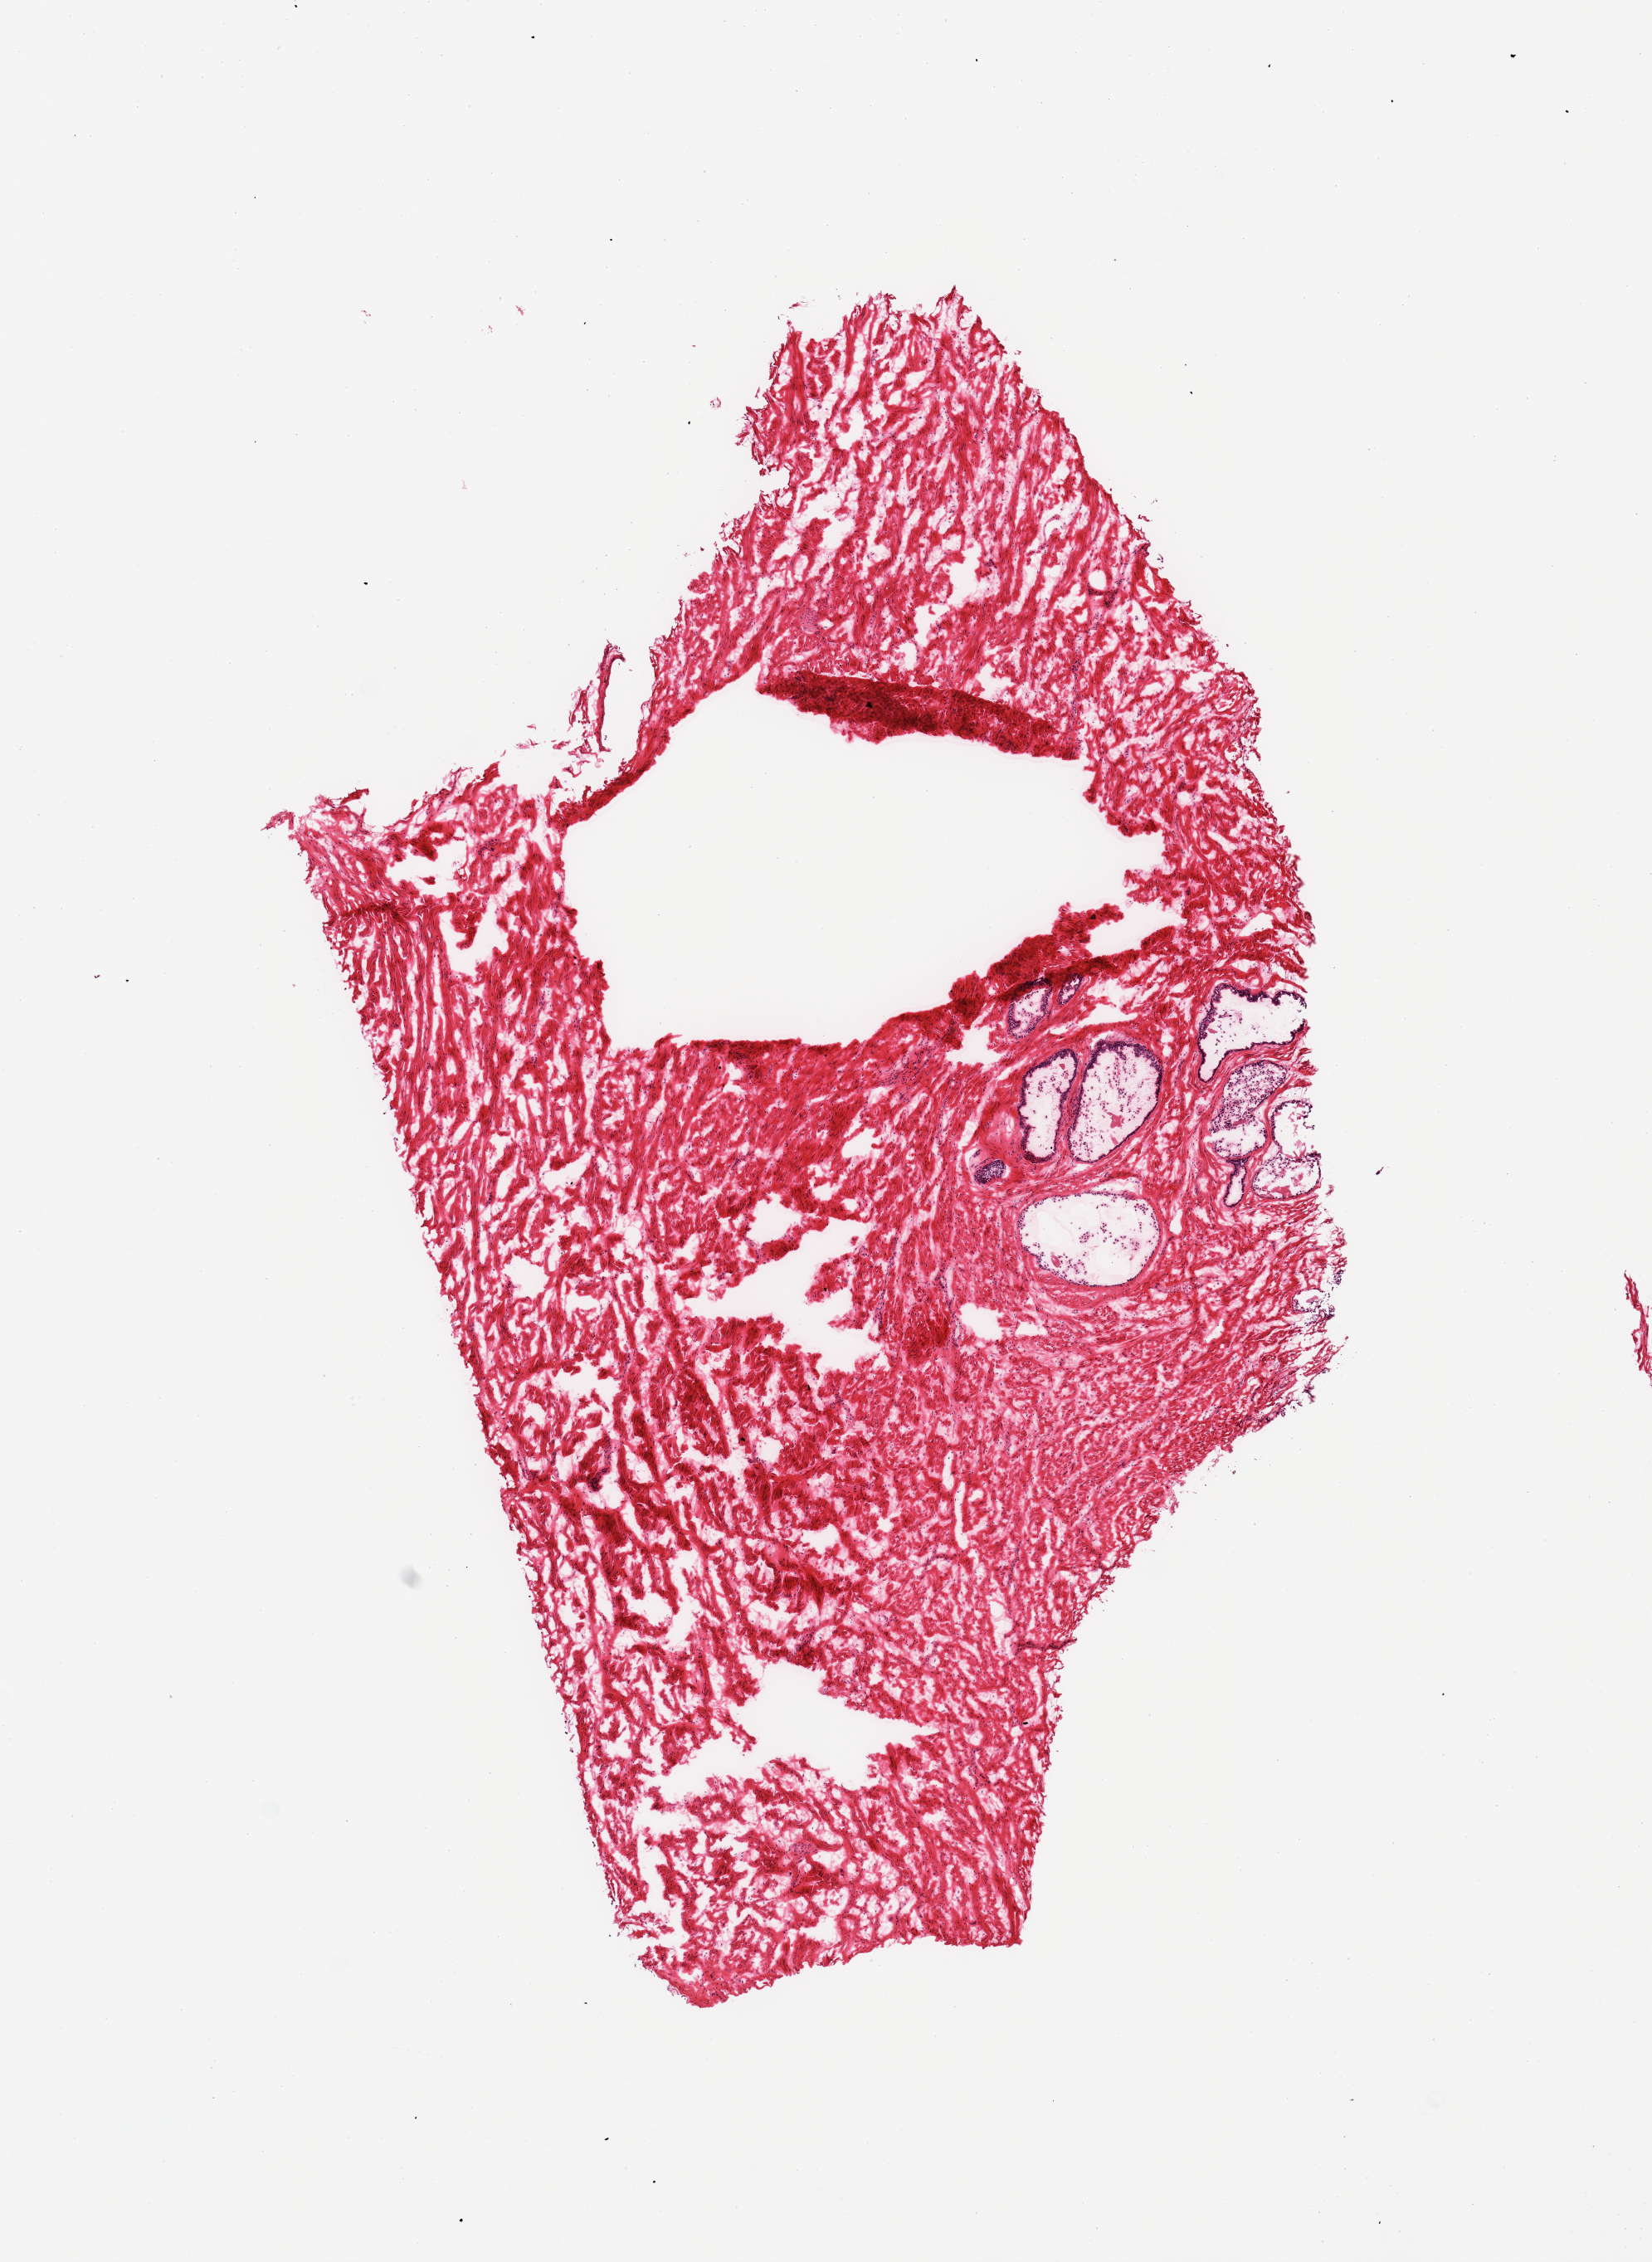
Whole-slide image, hematoxylin and eosin (H&E) stain — low-resolution overview of the scanned area, about 7.9 x 10.8 mm (slide scanned at 20x), frozen section (dry ice), target tissue: prostate, donor tissue sample. Donor sex: male.
Pathologist's review note for this sample: 1 piece.